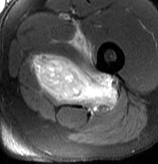
MRI of an extremity soft-tissue mass, one axial slice. Slice 59 of 70 in the series (ordered by position). T2-weighted fat-saturated. MR volume resampled by the dataset authors to the PET/CT grid (not the native acquisition matrix). 158 × 164 image matrix, field of view 154 × 160 mm. Male patient. Case-level facts recorded for this patient, not image findings: histological type: extraskeletal osteosarcoma; grade: high; site of the primary tumour: left adductur.
Outlined on this slice (expert contour drawn on MRI and transferred to this co-registered scan by the dataset authors):
- gross tumour volume (mass): bounding box (x1, y1, x2, y2) in pixels: (29, 23, 119, 109)